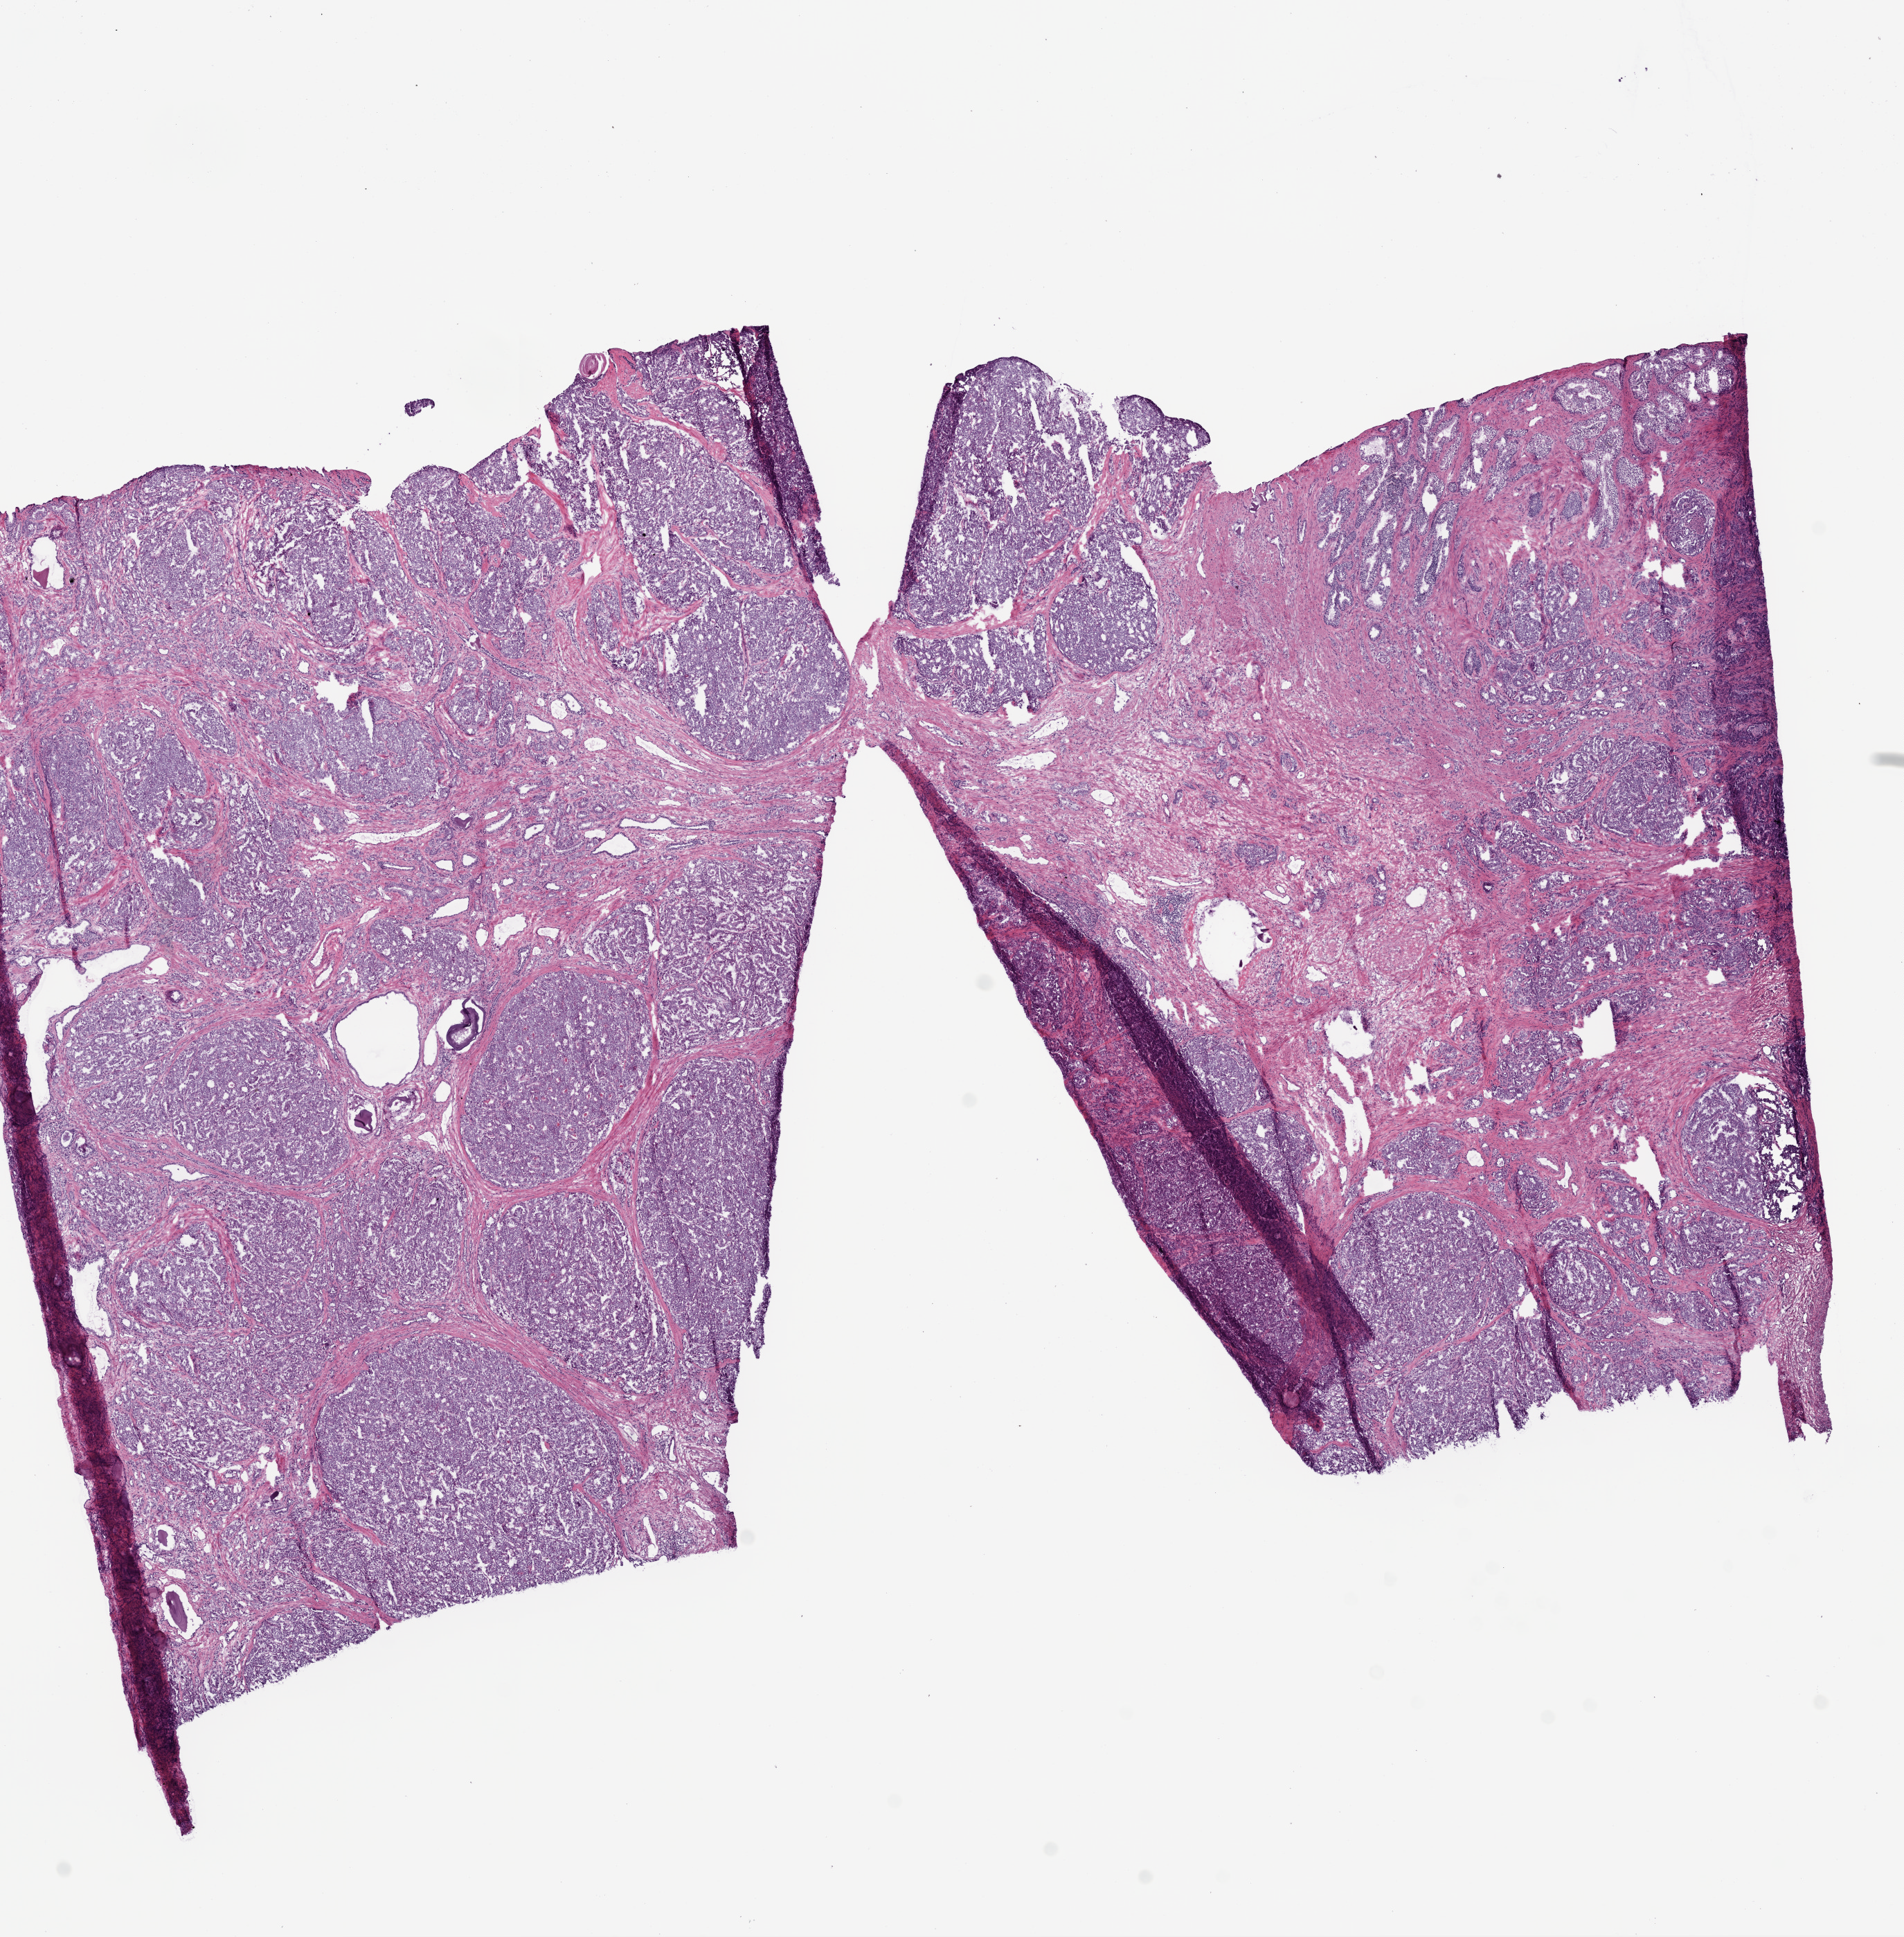
H&E-stained whole-slide image, a low-resolution overview of the entire scanned area, about 11.0 x 11.2 mm (acquisition: 20x scan), frozen section from the bottom of the tissue portion, prostate, primary tumour sample. Male patient; age at initial diagnosis 64 years. Gleason score: 8 (4+4). Slide review estimates, as recorded: tumour cells 60%, tumour nuclei 60%, normal cells 15%, stromal cells 25%, necrosis 0%. Infiltration values recorded for this section: lymphocyte infiltration 3%, monocyte infiltration 2%, neutrophil infiltration 0%.
Laterality: bilateral. Pathologic diagnosis: Acinar cell carcinoma (prostate gland). Lymph nodes positive (case pathology): 3 of 12 examined.